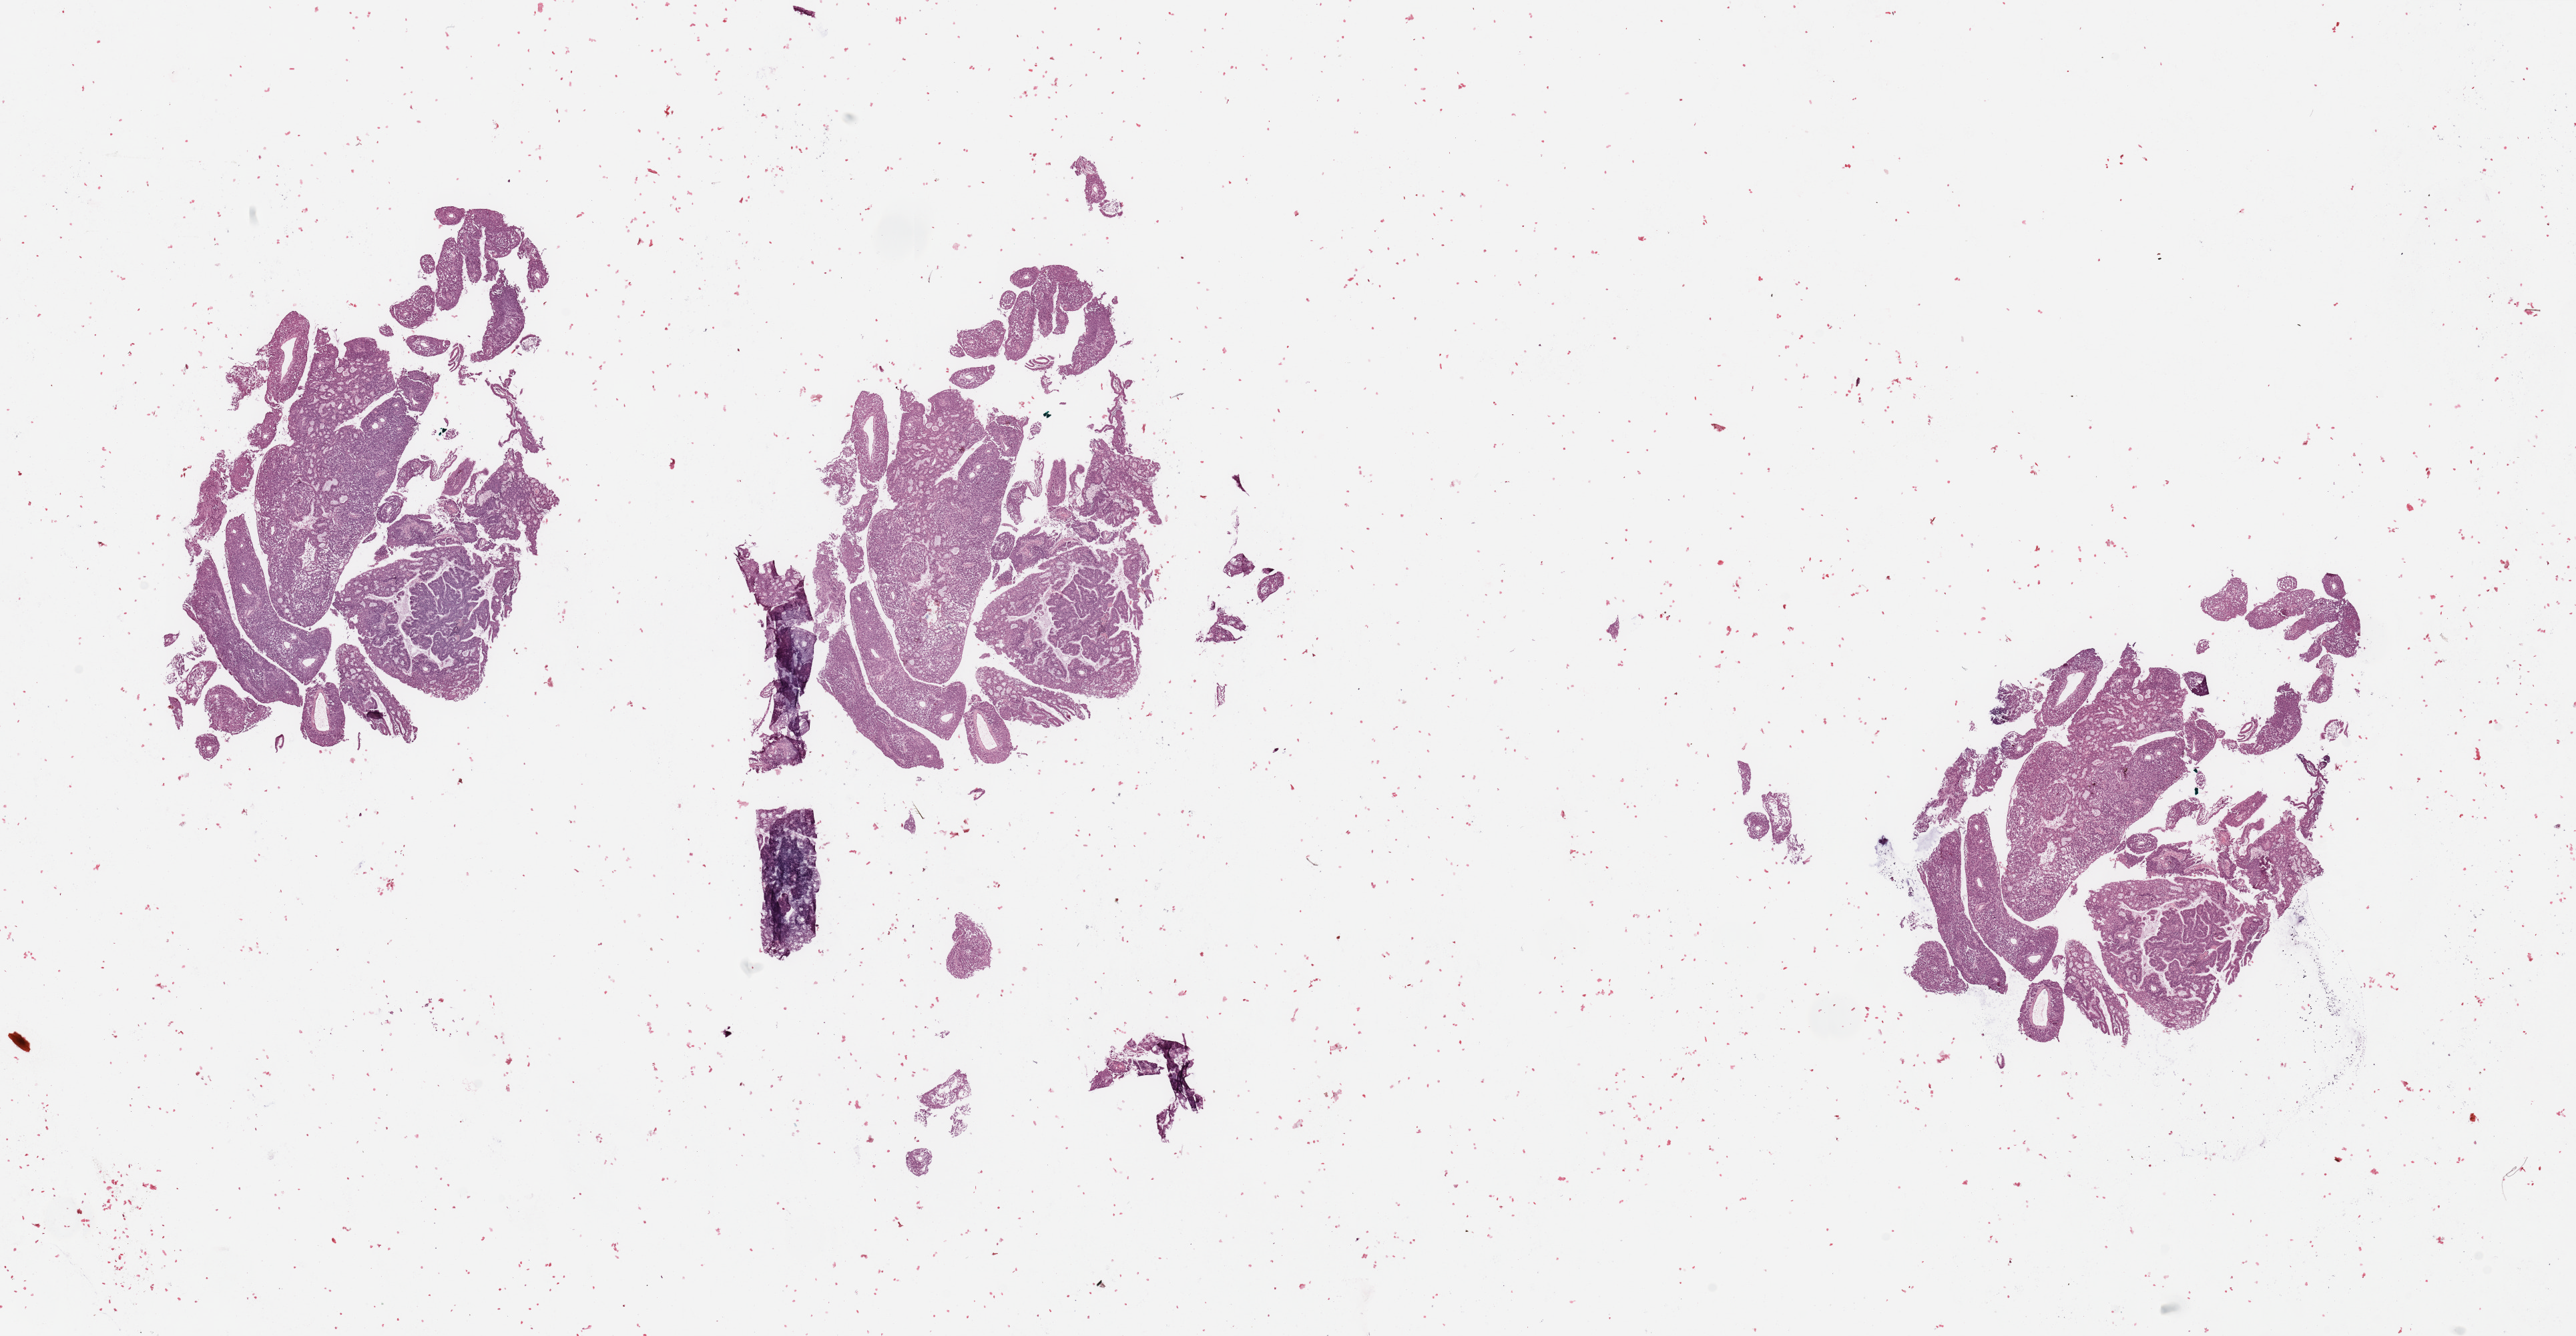
Digitized H&E tissue section (whole slide), whole scanned area (about 30.5 x 15.8 mm) shown as a low-resolution overview, tumour tissue sample, uterus. 56-year-old female patient. Histologic grade: G3 (poorly differentiated).
- primary tumour site (as recorded): anterior endometrium
- diagnosis: Endometrioid adenocarcinoma, NOS
- AJCC pathologic stage: IIIC1